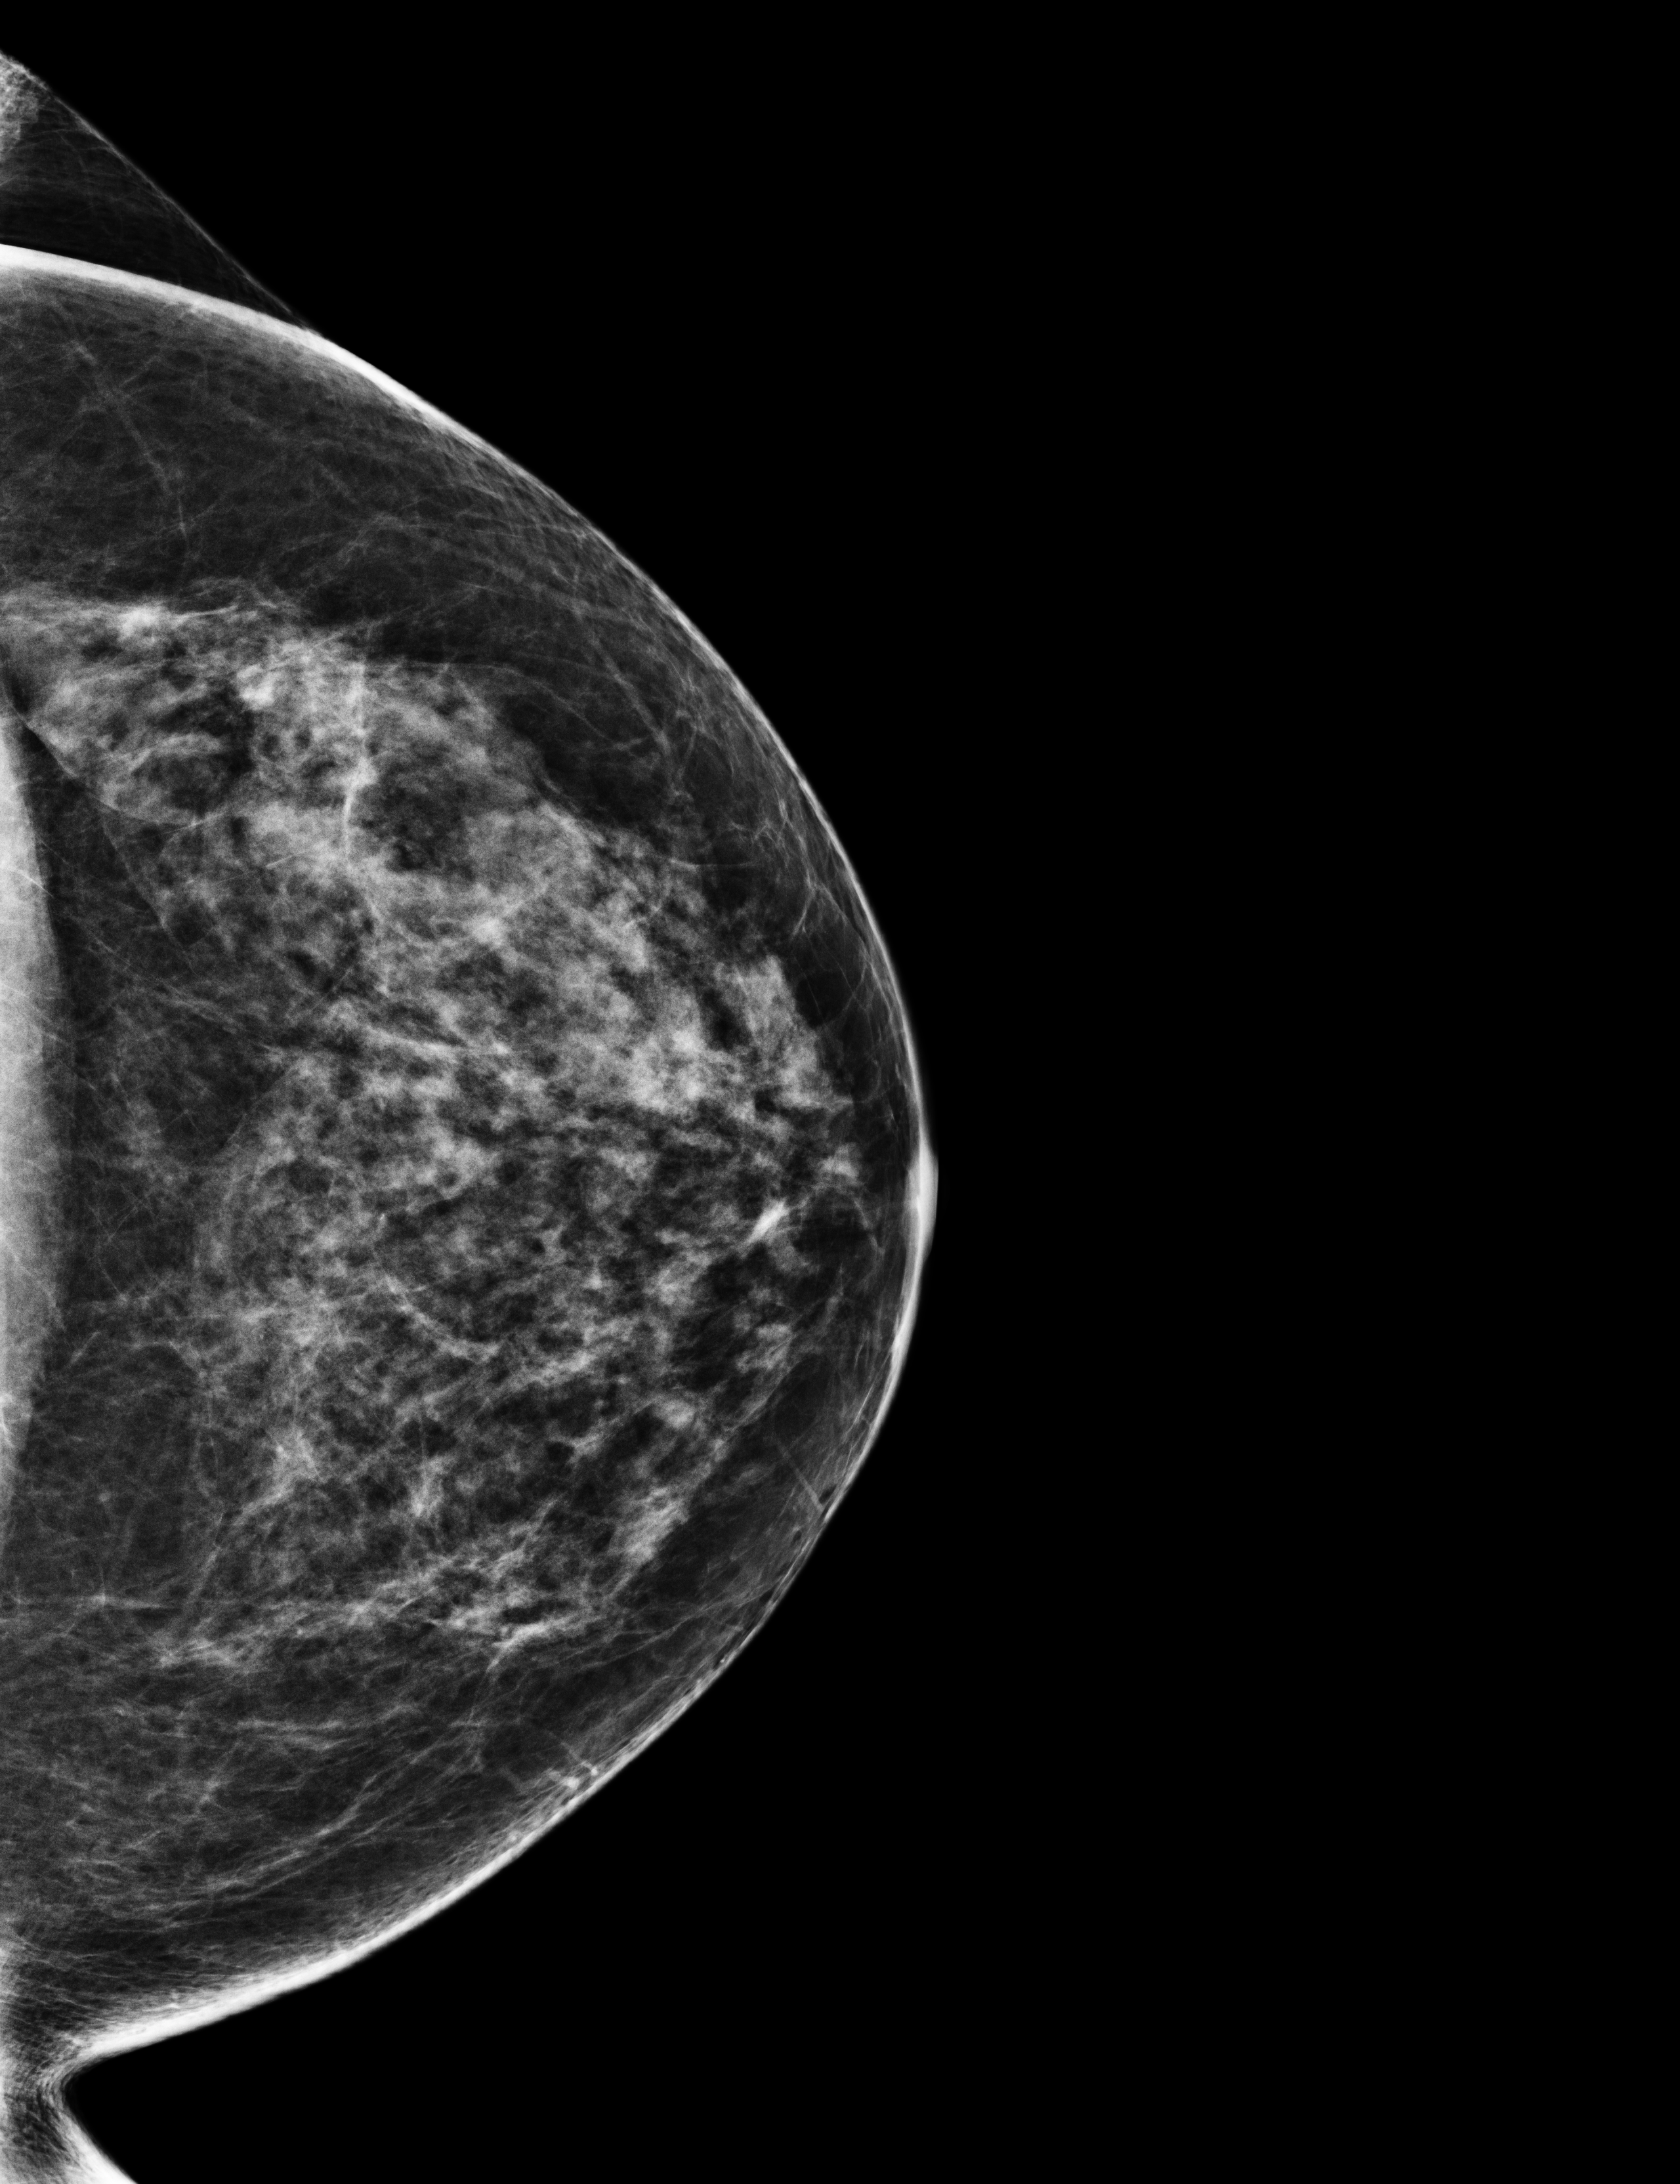
Full-field digital mammogram (FFDM); left breast; cranio-caudal projection; screening examination. Patient aged 60 years (female).
BI-RADS breast density category at the screening exam (both breasts, scale 1–4): 3. Final BI-RADS category for the screening round (tomosynthesis exam, both breasts): category 1. Recall: no recall after this screen.